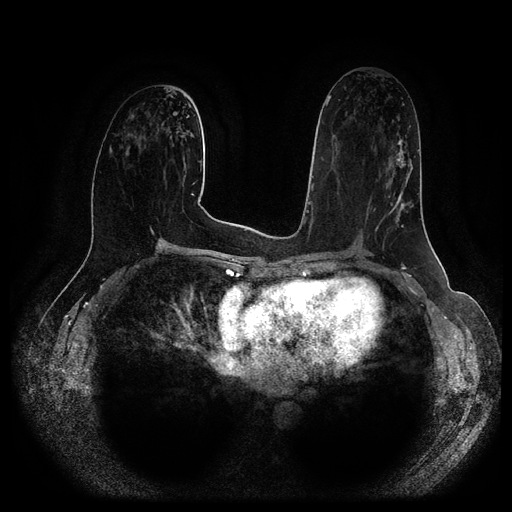
Breast MRI (dynamic contrast-enhanced, multi-phase), one axial slice. Slice 53 of 116 in the series (ordered by position). Dynamic contrast-enhanced series, time point 2 of 5 at this slice position (early post-contrast). 1.5 T. TE 2.6 ms, TR 5.2 ms. 2 mm slice thickness. 512 × 512 image matrix, field of view 380 × 380 mm. Patient: female, 57 years.
Annotated regions visible in this slice (semi-automatic segmentation, software-assisted and operator-edited):
- breast lesion (labelled 'tumour' in the annotation; benign lesions carry a separate 'benign' label): bounding box <375,135,416,232> (left, top, right, bottom; pixels)